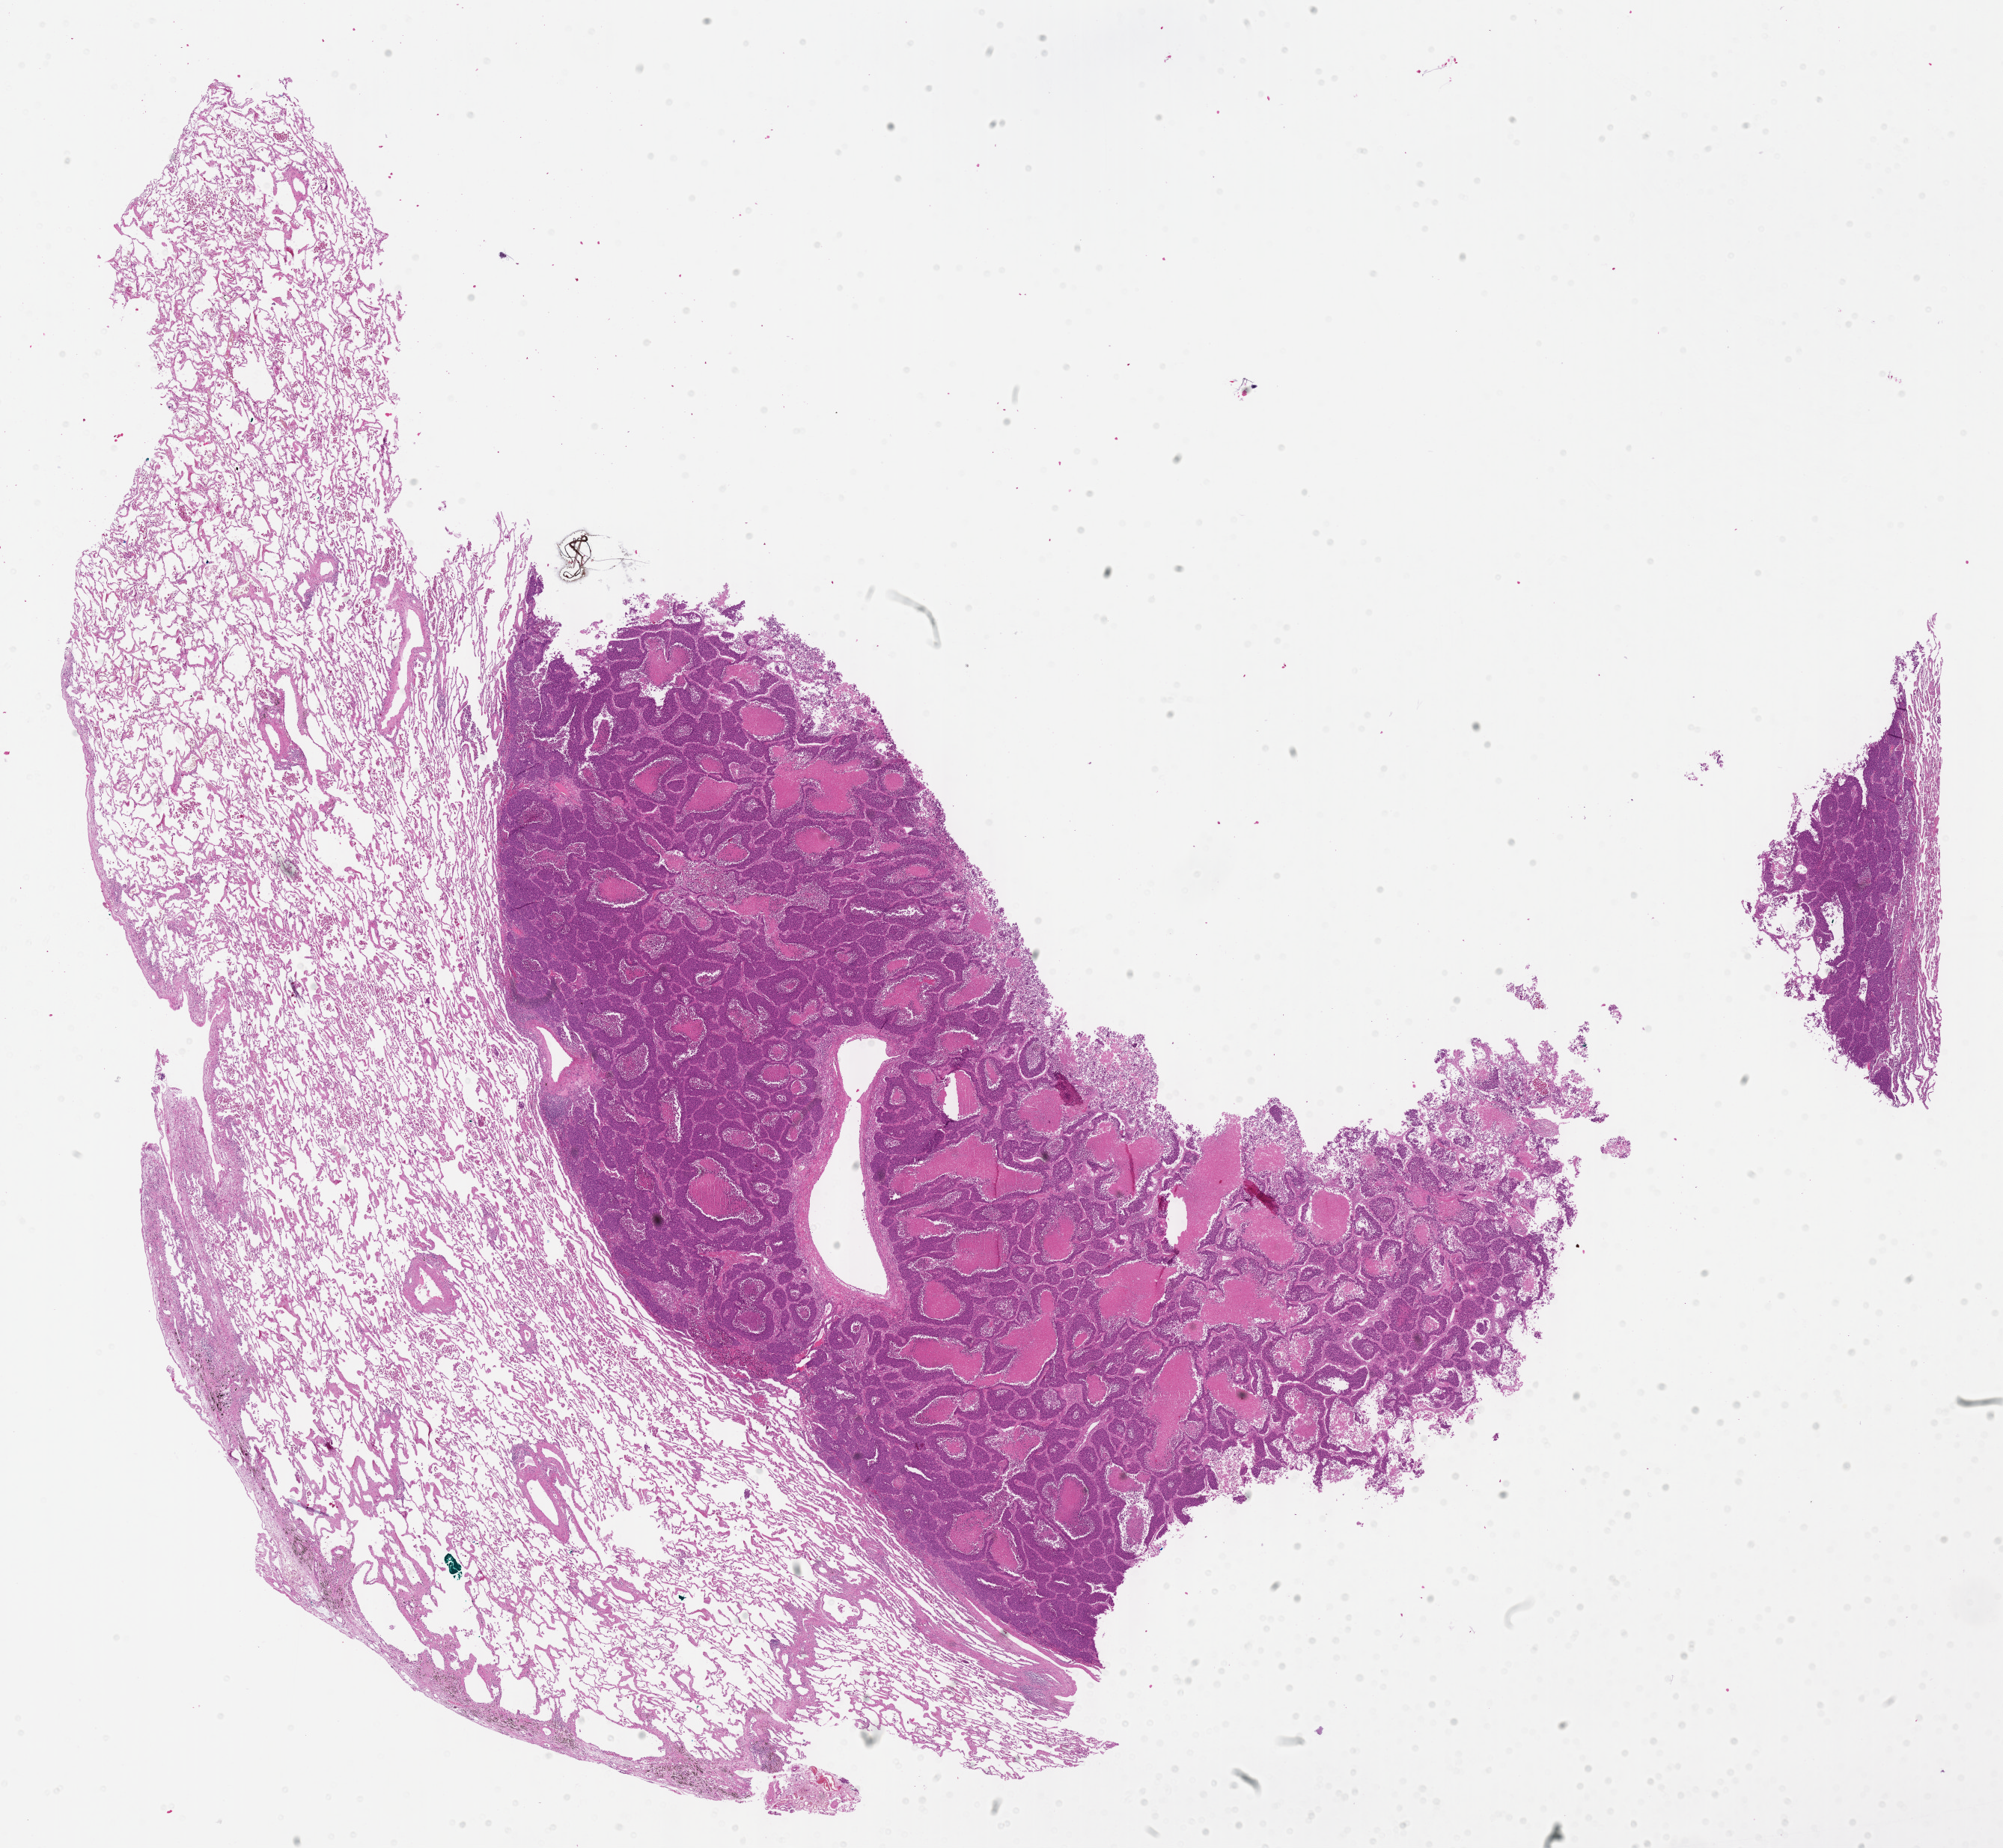
Whole-slide histology image, Hematoxylin and eosin (H&E) stained, whole scanned area (about 21.6 x 20.0 mm) shown as a low-resolution overview; formalin-fixed paraffin-embedded (FFPE) diagnostic section; sample: primary tumour, lung. Male patient; age at initial diagnosis 59 years.
AJCC pathologic stage: IIB (6th edition). TNM: T3 N0 M0. Pathologic diagnosis: Squamous cell carcinoma, NOS. Laterality: right.